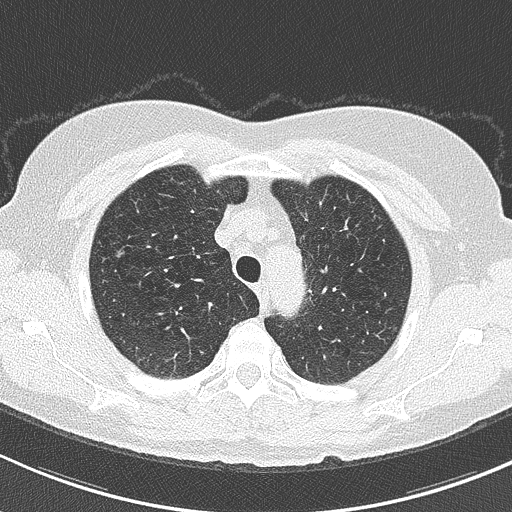
Axial slice from a low-dose chest CT screening exam. First (baseline) screen. Lung window (W 1500 / L -600 HU). 2 mm slice thickness. 120 kVp. Slice 38 of 202 in the series. 512 × 512 image matrix, field of view 312 × 312 mm. Female, age 60 years at enrolment. Former smoker at enrolment.
Expert reader's lesion annotation, box from (x=102, y=238) to (x=133, y=271) px. The exam's reader record, not a measurement of the box and not confirmed to be the same lesion: non-calcified nodule or mass ≥4 mm, right upper lobe, 4 × 4 mm, smooth margins, soft tissue attenuation. Official screen result: positive, change unspecified: nodule(s) >= 4 mm or enlarging nodule(s), mass(es), or other non-specific abnormalities suspicious for lung cancer. Later outcome: lung cancer diagnosed 216 days after this screen — acinar cell carcinoma, right upper lobe, well differentiated (G1), stage IA (AJCC 6th edition), 7 mm at pathology.